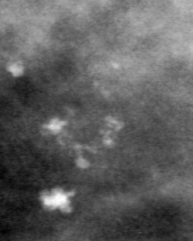
Cropped region of a digitized screen-film mammogram centred on a radiologist-marked abnormality, right breast, CC view, BI-RADS breast density category 3 (scale 1–4).
- Finding: calcifications, morphology dystrophic, distribution clustered; BI-RADS assessment category 3; pathology result (as recorded, not read from the image): benign.